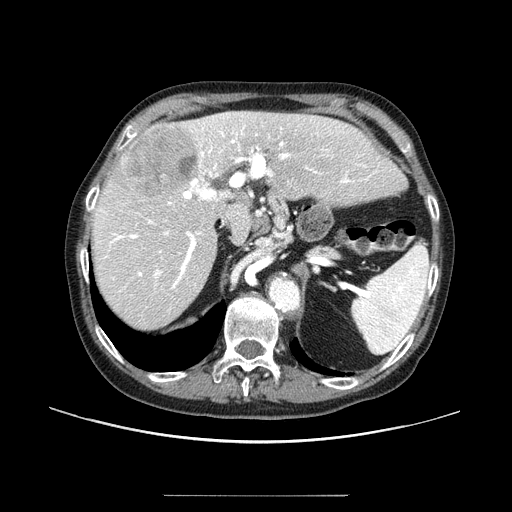
Contrast-enhanced abdominal CT (liver protocol), one axial slice; position 62 of 91 along the scan axis; 100 kVp; one of 2 acquisitions stored at this slice position; soft-tissue window (W 400 / L 40 HU); 2.5 mm slice thickness; 512 × 512 image matrix, field of view 400 × 400 mm. Case-level facts recorded for this patient, not image findings: diagnosis: hepatocellular carcinoma (patient treated with transarterial chemoembolisation; whether this scan precedes or follows treatment is not stated here); TNM stage (as recorded): Stage-I; Child-Pugh class: A.
Annotated regions visible in this slice (semi-automatically segmented with operator editing):
- liver parenchyma outside the tumour (the mass and vessels are separate outlines, so this box may not span the whole liver): bounding box (x1, y1, x2, y2) in pixels: (92, 110, 406, 328)
- mass: (112, 125, 198, 198)
- liver vessels: (98, 113, 380, 289)